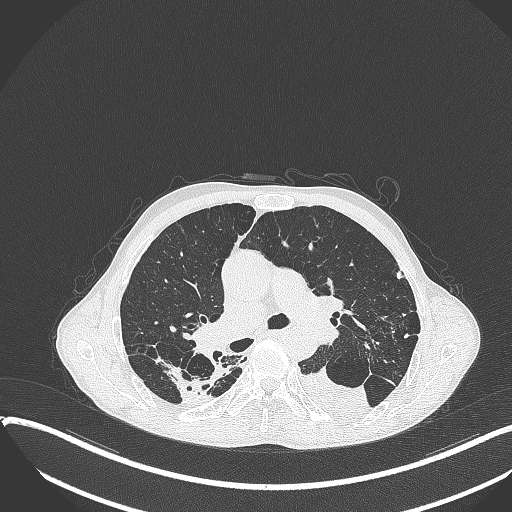
Chest CT, one axial slice; position 239 of 401 along the scan axis; reconstruction kernel B70f; 120 kVp; lung window (W 1500 / L -600 HU); 512 × 512 image matrix. Male patient, age 57 years. From the clinical record (not read from this slice): clinical TNM (as recorded): T4 N0 M0.
Structures marked on this image (rectangle marked by the reading radiologist):
- lung tumour (recorded histology: squamous cell carcinoma): box from (x=294, y=365) to (x=369, y=421) px